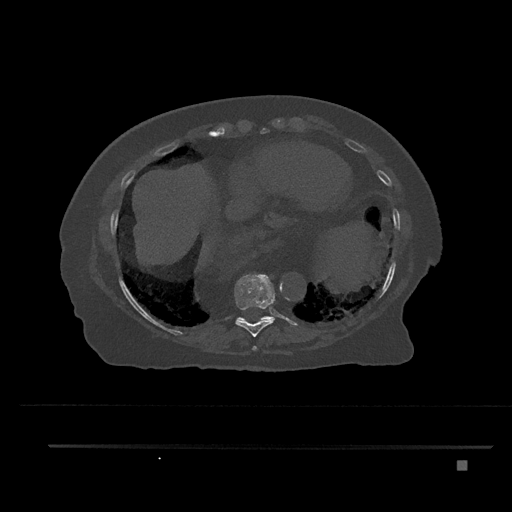
CT including the spine, one axial slice. Slice 390 of 797 in the series (ordered by position). Reconstruction kernel Br40s/3. 120 kVp. Bone window (W 1800 / L 400 HU). 0.5 mm slice thickness. 512 × 512 image matrix, field of view 437 × 437 mm. Female patient, age 76 years. Case-level facts recorded for this patient, not image findings: primary cancer: lung.
Outlined on this slice (semi-automatic segmentation, software-assisted and operator-edited):
- T10 vertebra: bounding box (x1, y1, x2, y2) in pixels: (237, 316, 272, 320)
- T8 vertebra: (252, 346, 257, 351)
- T9 vertebra: (234, 274, 275, 337)